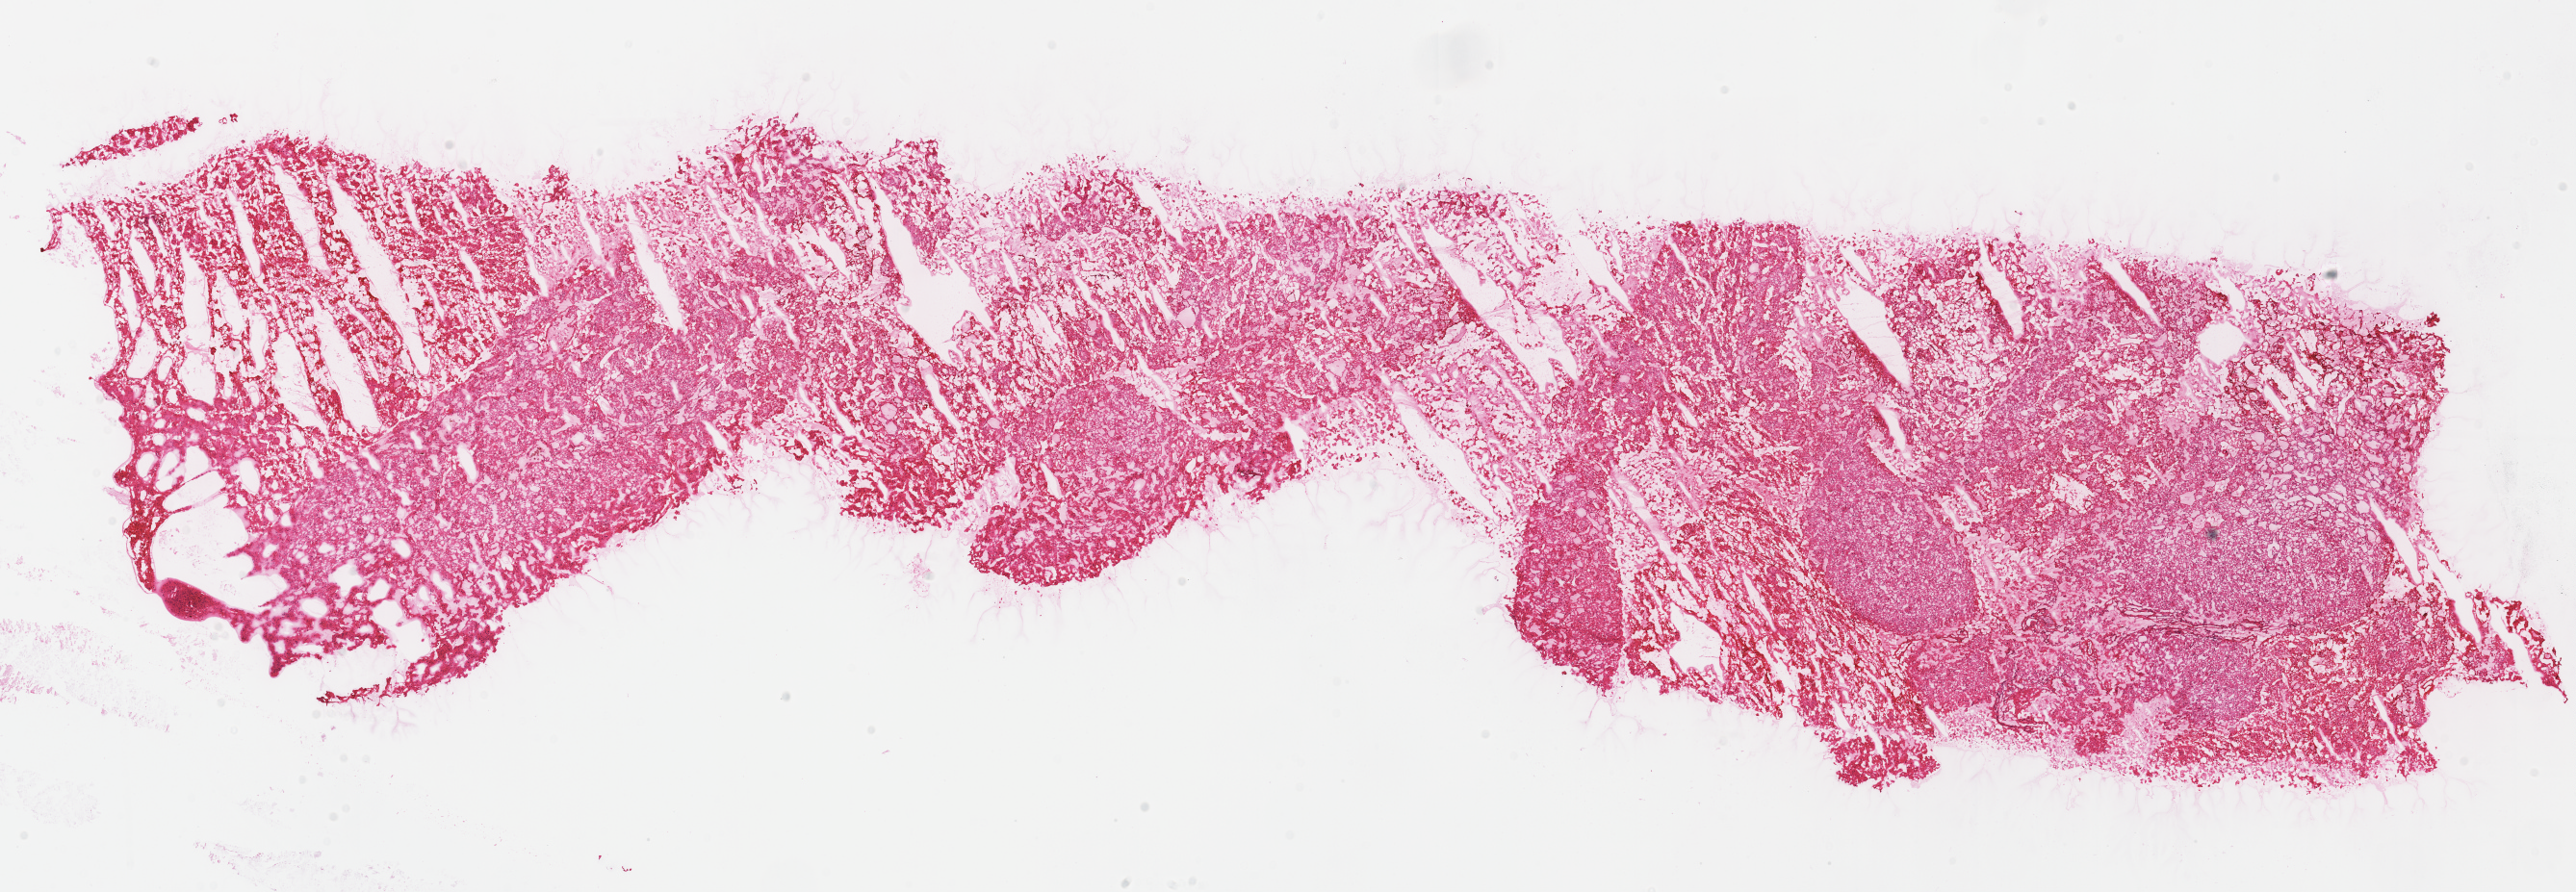
H&E whole-slide image, whole scanned area (about 21.0 x 7.3 mm) shown as a low-resolution overview, frozen section from the top of the tissue portion, kidney, primary tumour sample. Female, age 74 years at initial diagnosis. Slide review estimates, as recorded: tumour cells 90%, tumour nuclei 90%, normal cells 0%, stromal cells 10%, necrosis 0%.
AJCC pathologic stage: I (7th edition). Lymph nodes positive (case pathology): 0 of 1 examined. TNM: T1b N0 M0. Histologic diagnosis: Renal cell carcinoma, chromophobe type.